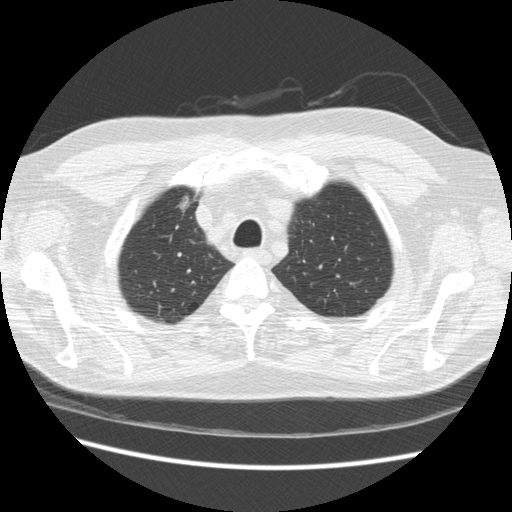
Low-dose screening chest CT, one axial slice; position 193 of 234 along the scan axis; reconstruction kernel STANDARD; 120 kVp; lung window (W 1500 / L -600 HU); 512 × 512 image matrix.
Structures marked on this image (expert manual segmentation):
- lesion 1 (tumor, upper lobe of right lung): box from (x=178, y=194) to (x=189, y=212) px